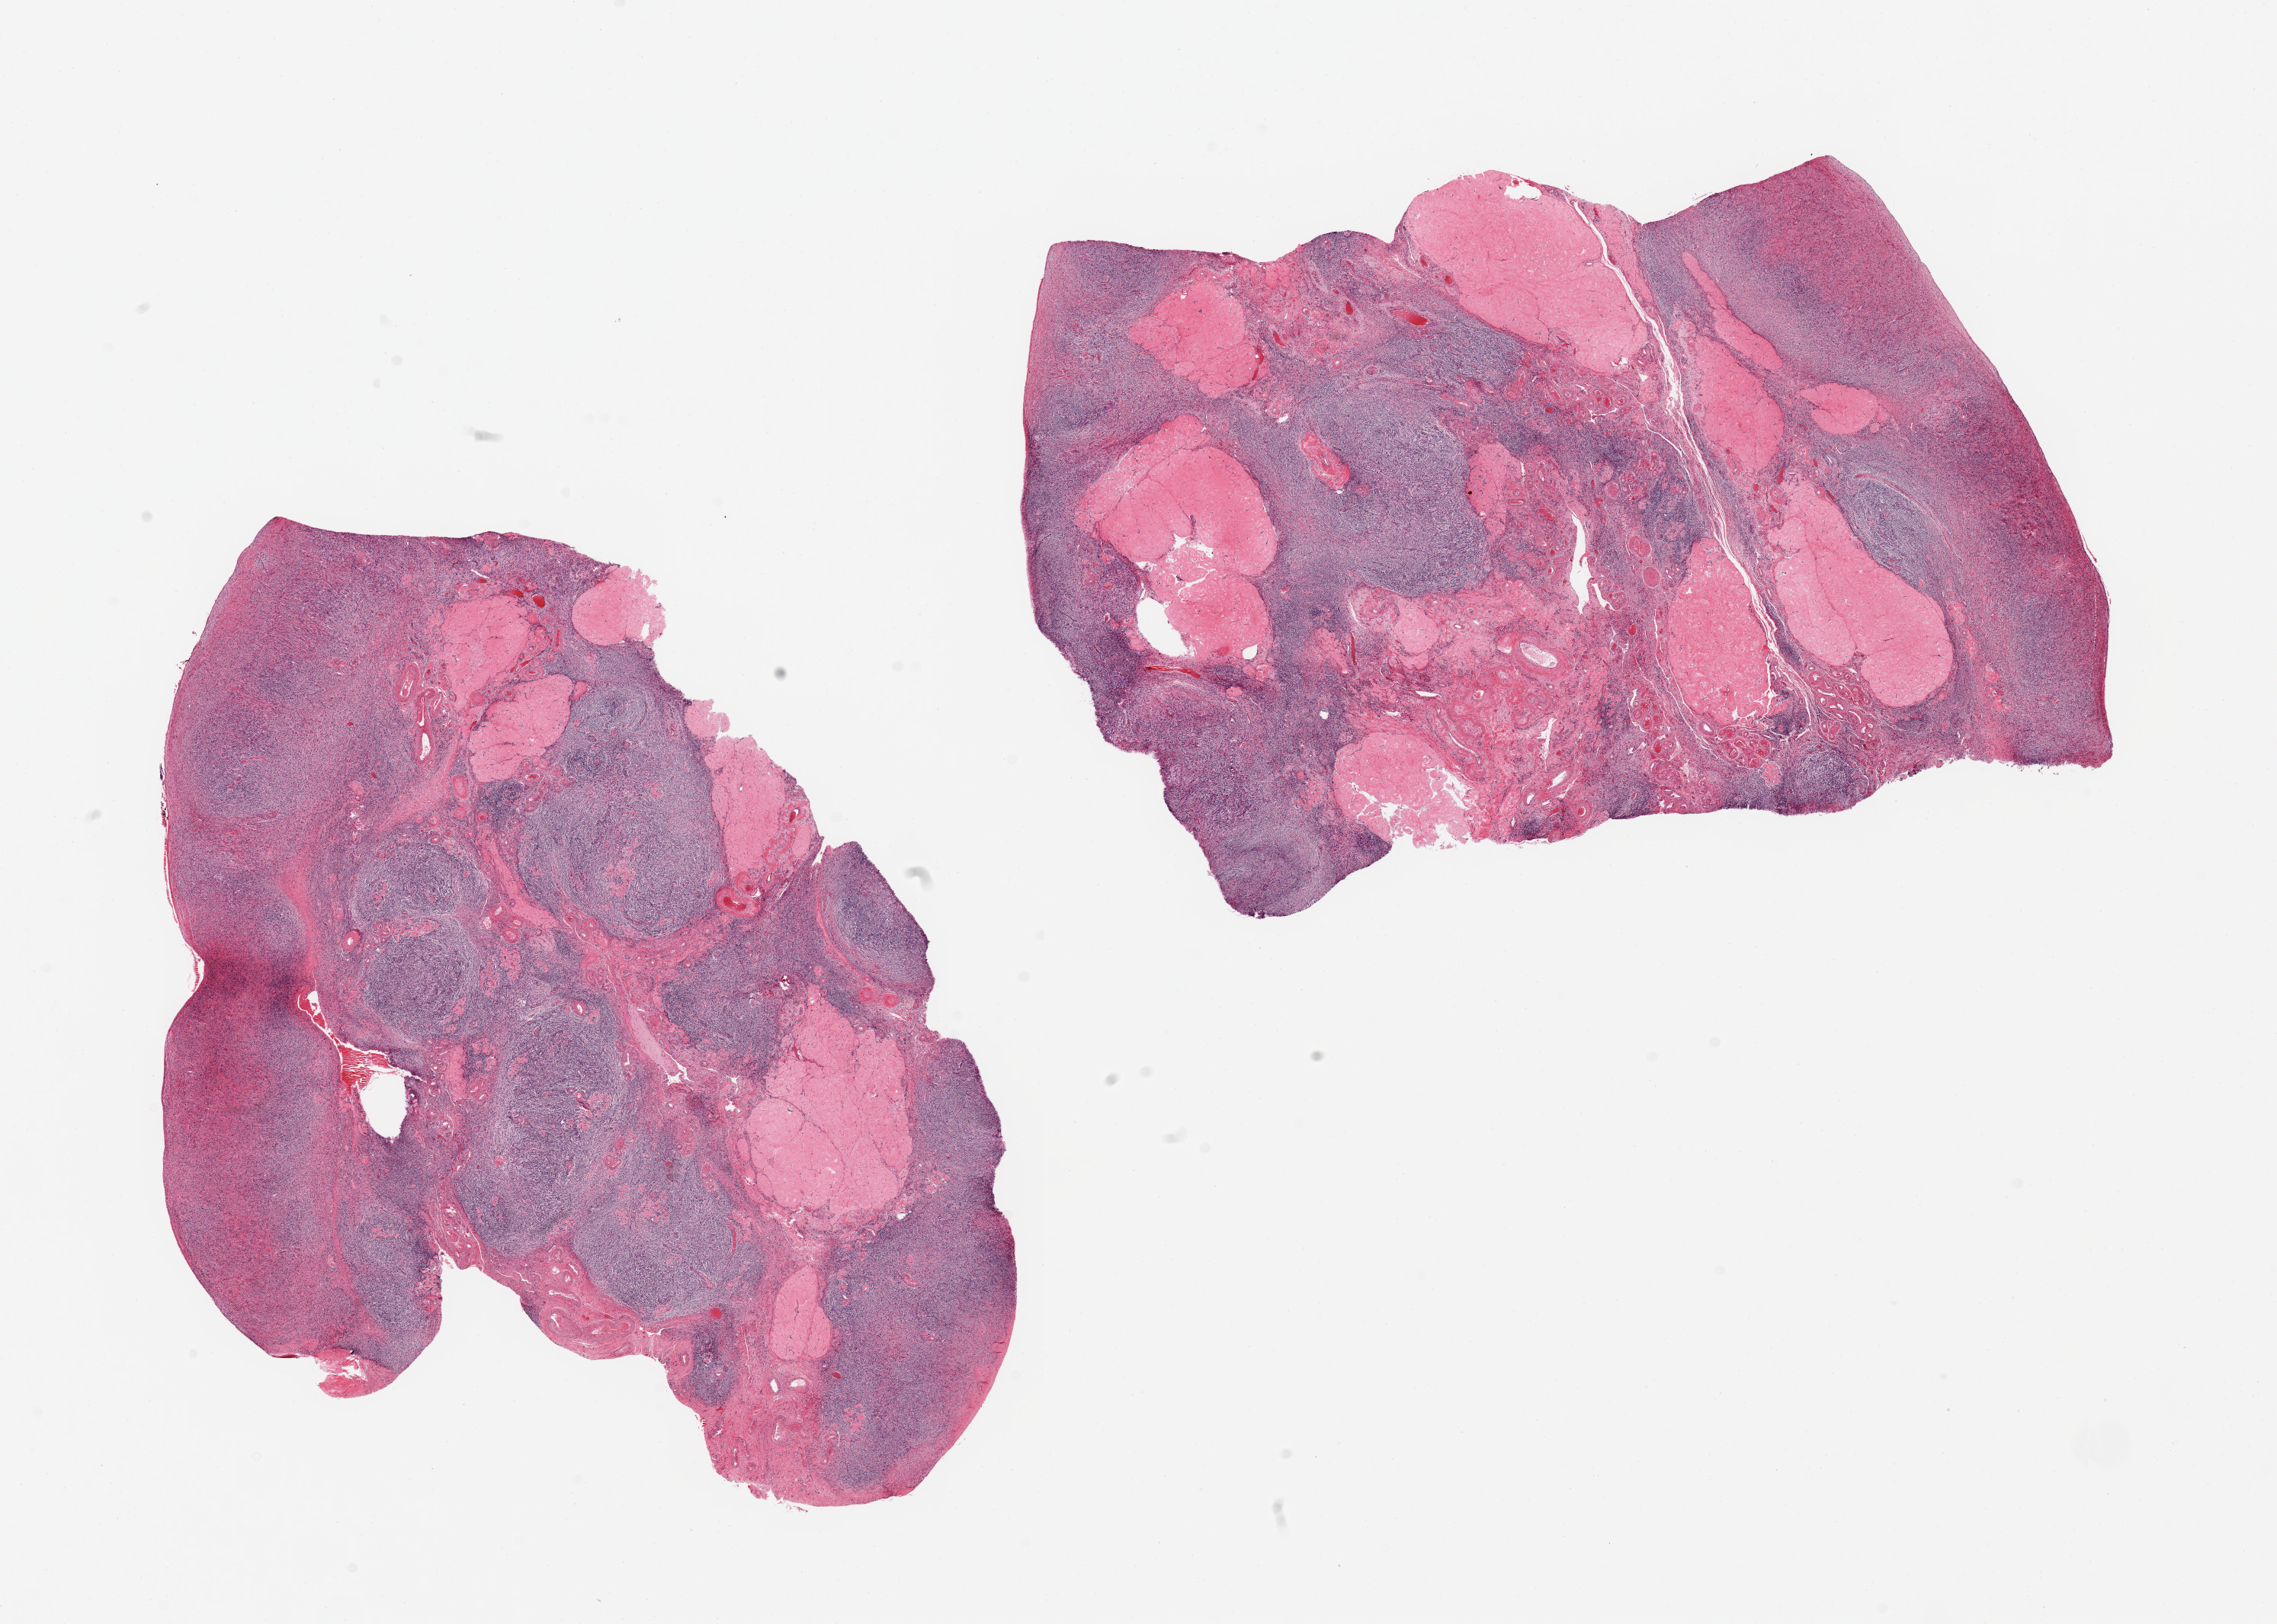
Haematoxylin and eosin whole-slide image, brightfield, whole scanned area (about 23.6 x 16.9 mm) shown as a low-resolution overview; PAXgene-fixed paraffin-embedded (PFPE) section; section of ovary (target tissue); donor tissue sample.
Reviewer comment on this tissue sample: 2 pieces; multiple corpora albicantia.